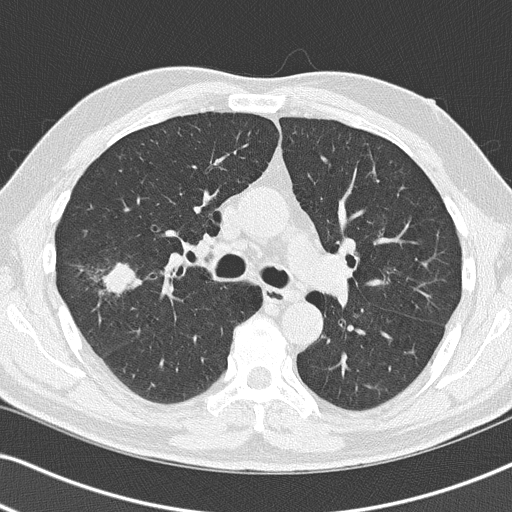
Chest CT (low-dose screening protocol), one axial image; baseline screening round; lung window (W 1500 / L -600 HU); 2 mm slice thickness; lung (sharp) reconstruction kernel (B50f); slice 60 of 140 in the series; 512 × 512 image matrix. Male participant, aged 67 years at enrolment. Former smoker at enrolment.
Expert-annotated lung lesion, bounding box [x1, y1, x2, y2] px = [71, 253, 147, 319]. Reader record for this screening exam (exam-level; its link to the box is not recorded): non-calcified nodule or mass ≥4 mm, right upper lobe, 26 × 24 mm, spiculated (stellate) margins, soft tissue attenuation. Later outcome: lung cancer diagnosed 49 days after this screen — squamous cell carcinoma, NOS, right upper lobe, poorly differentiated (G3), stage IA (AJCC 6th edition), 27 mm at pathology.